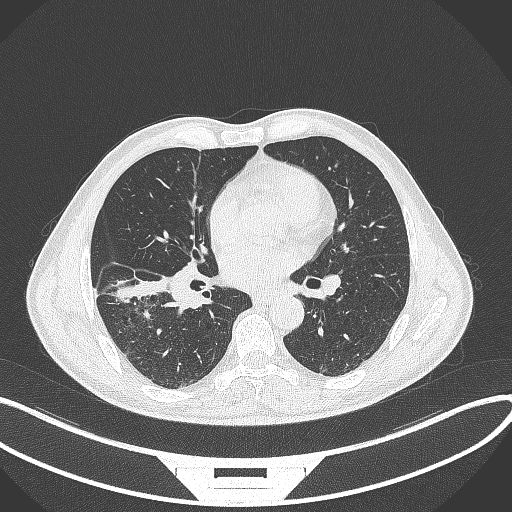
Chest CT, one axial slice. Position 173 of 364 along the scan axis. 120 kVp. Lung window (W 1500 / L -600 HU). 1 mm slice thickness. 512 × 512 image matrix, field of view 400 × 400 mm. Male patient, age 58 years. Case-level facts recorded for this patient, not image findings: clinical TNM (as recorded): T3 N0 M0.
Outlined on this slice (bounding box drawn by a radiologist):
- lung tumour (recorded histology: squamous cell carcinoma): box from (x=110, y=275) to (x=173, y=305) px